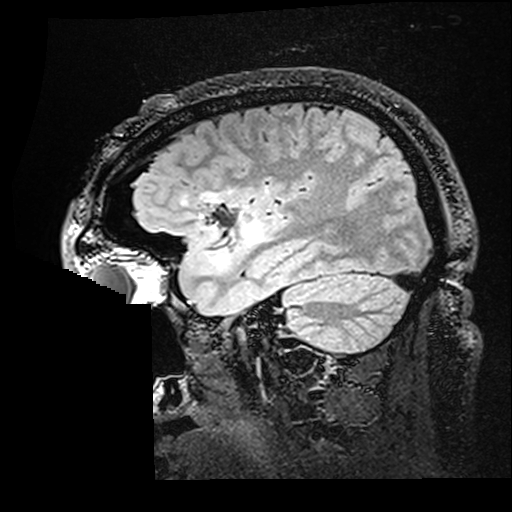
Brain MRI from a brain-tumour surgery series, one sagittal slice. Position 125 of 176 along the scan axis. T2 FLAIR. 512 × 512 image matrix, field of view 250 × 250 mm. Case-level facts recorded for this patient, not image findings: histopathology: Astrocytoma; WHO grade: 2; IDH mutation: yes.
Structures marked on this image (manually delineated by an expert):
- residual tumour: box from (x=184, y=193) to (x=264, y=255) px